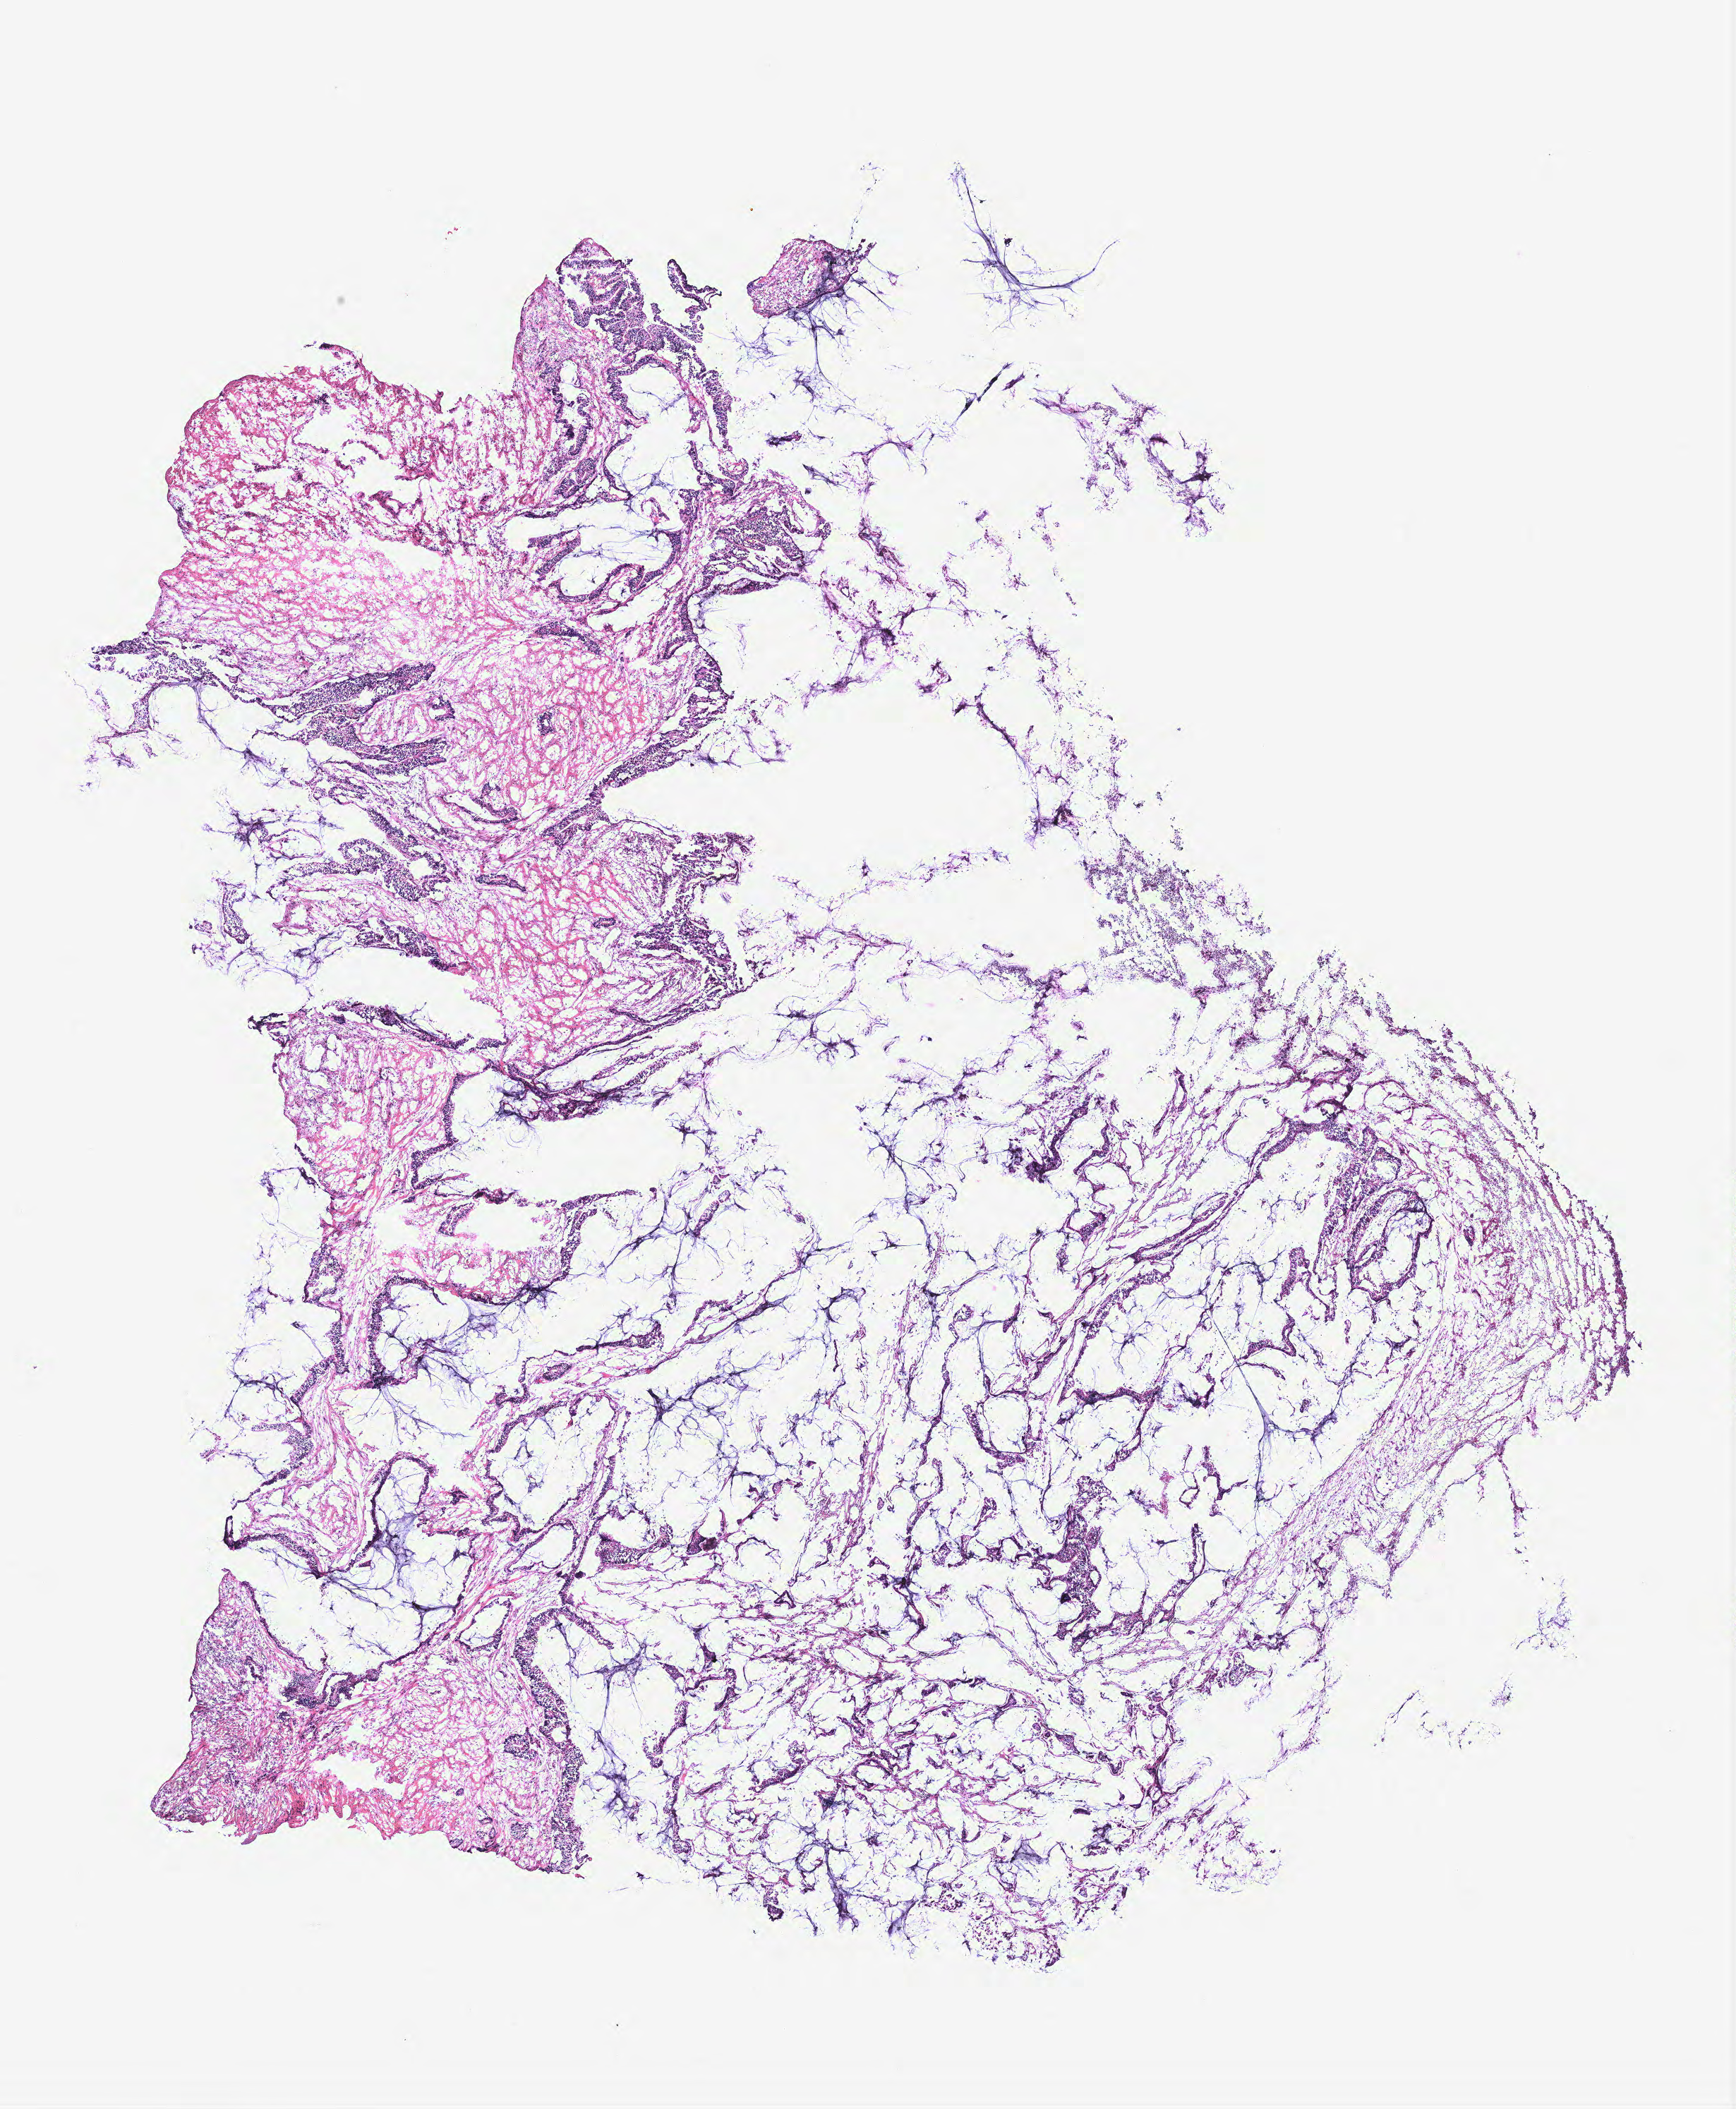
Hematoxylin and eosin (H&E) stained whole-slide image, a low-resolution overview of the entire scanned area, about 9.8 x 12.0 mm; colon, tissue type not recorded.
- patient diagnosis (cohort enrolment): colon cancer (colon)